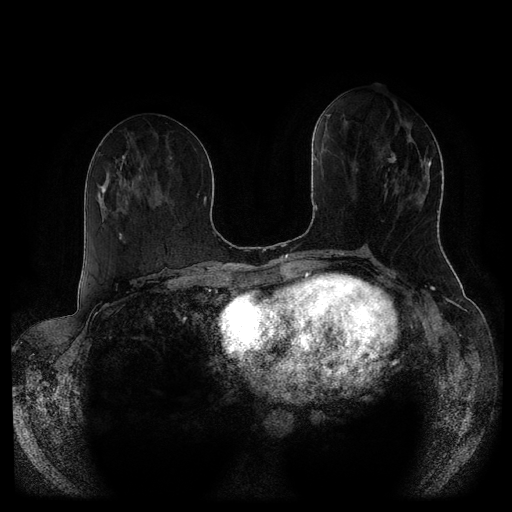
Breast MRI (dynamic contrast-enhanced, multi-phase), one axial slice. Position 43 of 116 along the scan axis. Dynamic contrast-enhanced series, time point 2 of 5 at this slice position (early post-contrast). 1.5 T. TE 2.6 ms, TR 5.3 ms. 512 × 512 image matrix, field of view 370 × 370 mm. Patient: female, 51 years.
Outlined on this slice (semi-automatically segmented with operator editing):
- breast lesion (labelled 'tumour' in the annotation; benign lesions carry a separate 'benign' label): box from (x=378, y=153) to (x=396, y=201) px